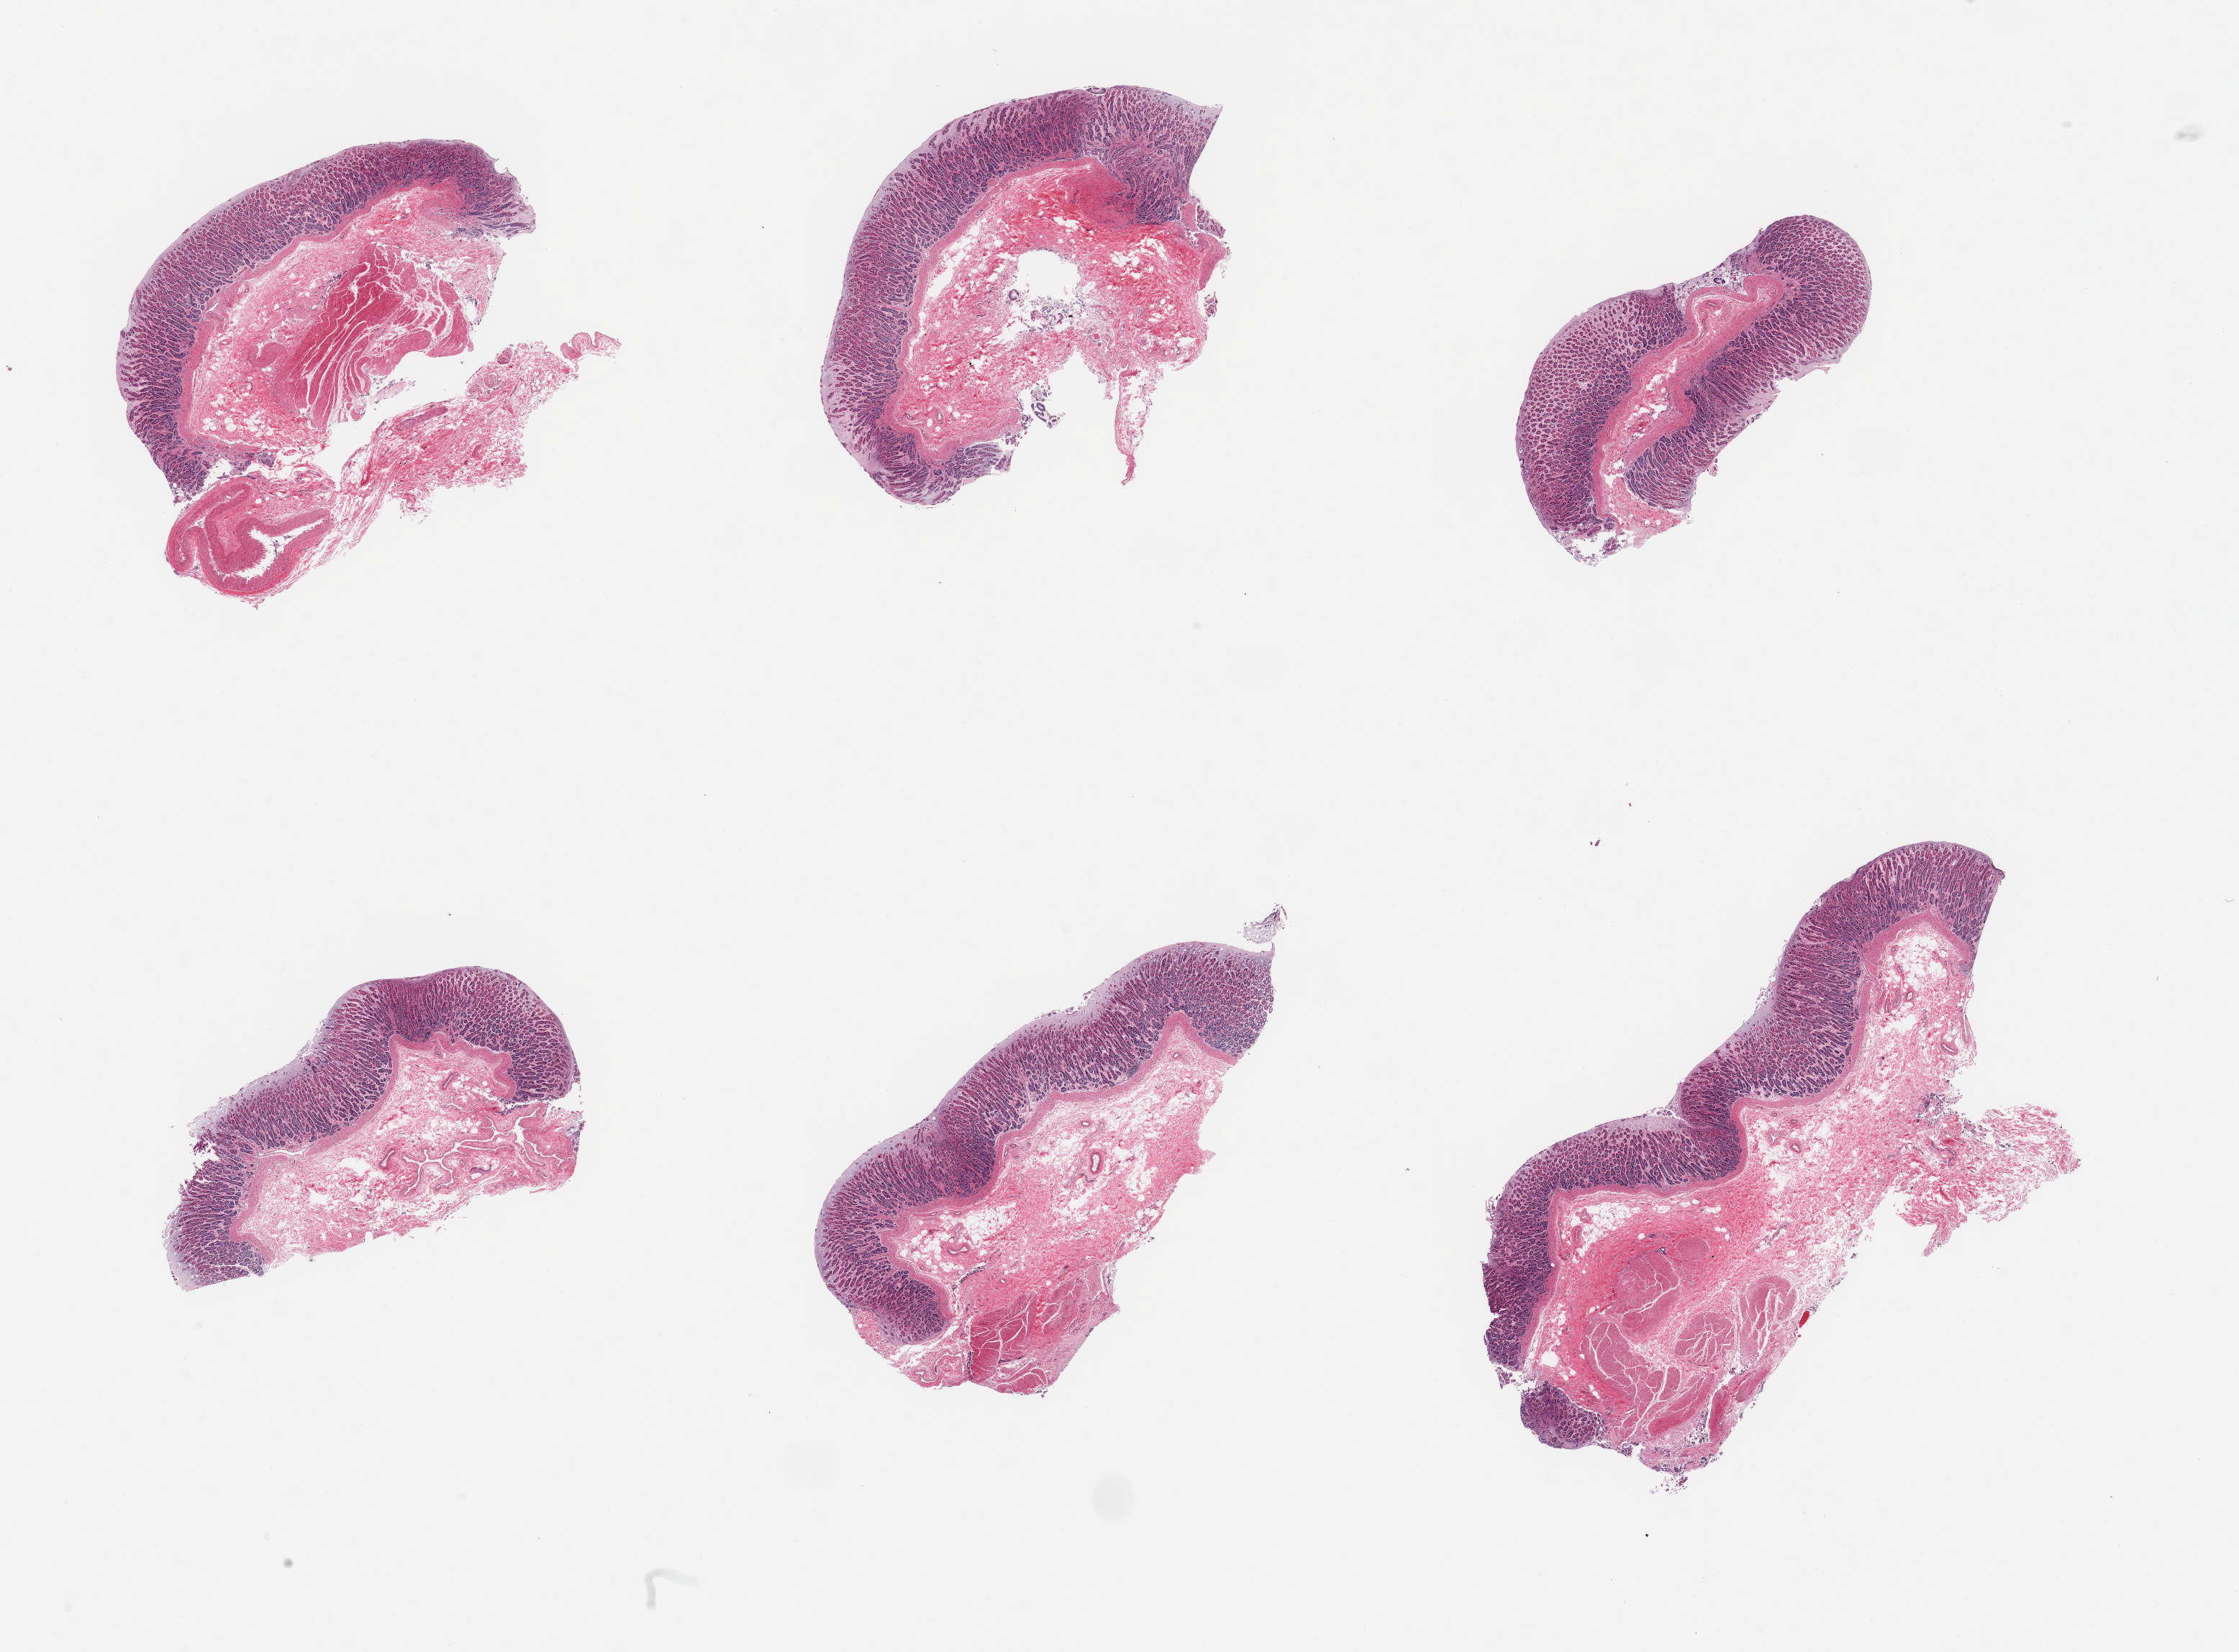
Whole-slide image, haematoxylin and eosin stain, brightfield, shown as a low-resolution overview of the whole scanned area (about 24.6 x 18.2 mm). PAXgene-fixed, paraffin-embedded tissue. Sampled site (target tissue): stomach. Donor tissue sample. Male donor.
Pathologist's review note for this sample: 6 pieces; mild to moderate autolysis of gastric mucosa; 3 sections contain muscularis.